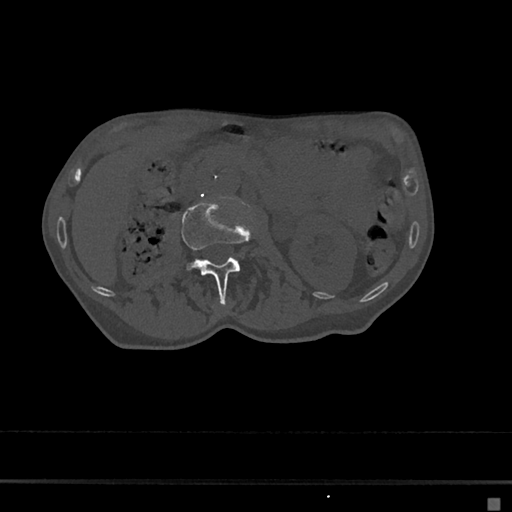
CT including the spine, one axial slice; position 7 of 797 along the scan axis; bone window (W 1800 / L 400 HU); 0.5 mm slice thickness; 512 × 512 image matrix. Female patient, age 68 years. Case-level facts recorded for this patient, not image findings: primary cancer: renal.
Outlined on this slice (semi-automatically segmented with operator editing):
- L2 vertebra: bounding box [x1, y1, x2, y2] px = [181, 200, 256, 303]